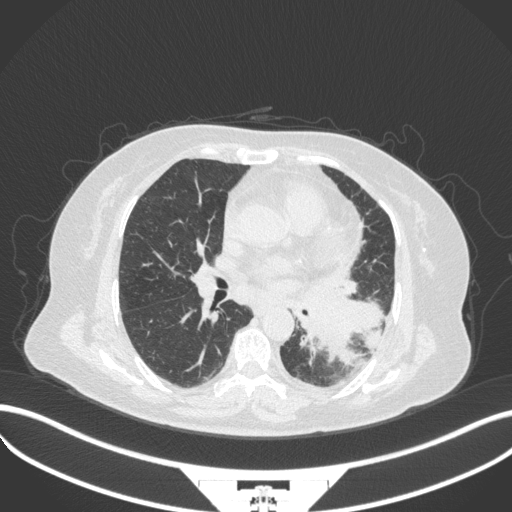
Chest CT, one axial slice; position 176 of 328 along the scan axis; reconstruction kernel B31f; 120 kVp; lung window (W 1500 / L -600 HU); 512 × 512 image matrix, field of view 400 × 400 mm. Female patient, age 69 years. Case-level facts recorded for this patient, not image findings: clinical TNM (as recorded): T2b N3 M1.
Outlined on this slice (bounding box drawn by a radiologist):
- lung tumour (recorded histology: adenocarcinoma): bounding box [x1, y1, x2, y2] px = [301, 291, 388, 361]